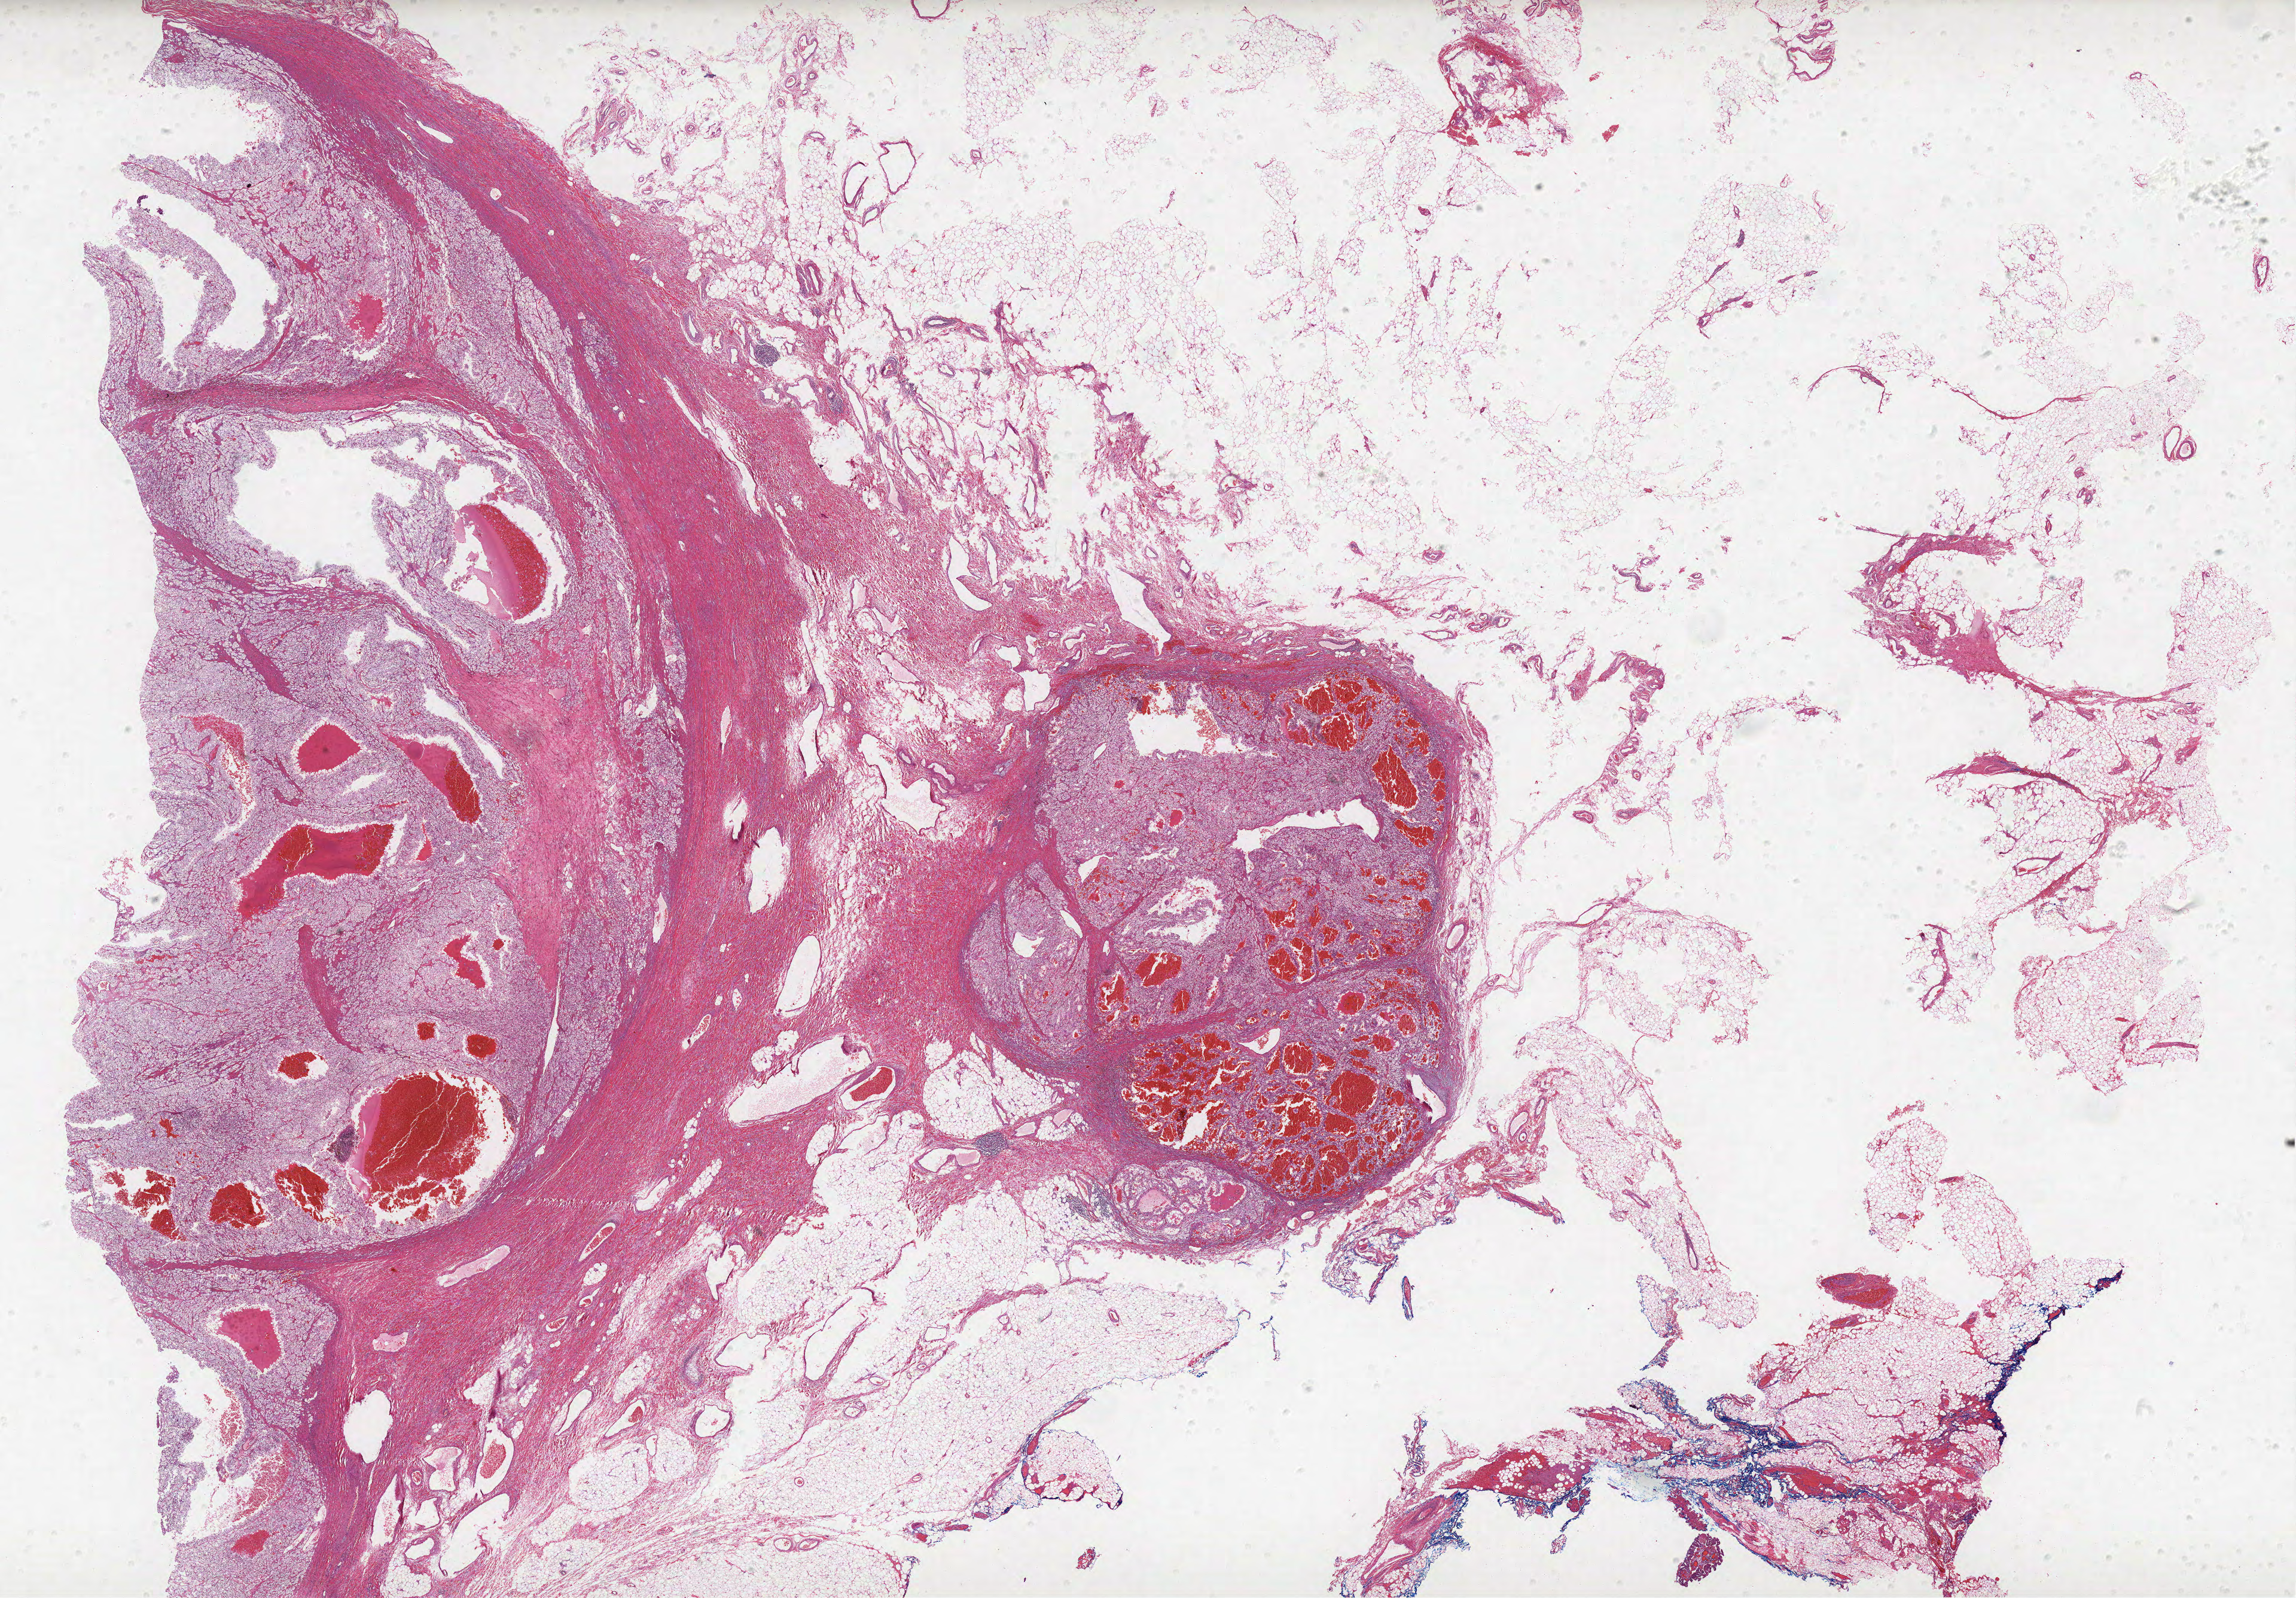
Whole-slide histology image, H&E-stained, whole scanned area (about 30.7 x 21.4 mm, slide scanned at 40x) shown as a low-resolution overview. Formalin-fixed paraffin-embedded (FFPE) diagnostic section. Primary tumour sample from the kidney. Female patient; age at initial diagnosis 43 years. Histologic grade: G3 (poorly differentiated).
Laterality: left. AJCC pathologic stage: III. Diagnosis: Clear cell adenocarcinoma, NOS.